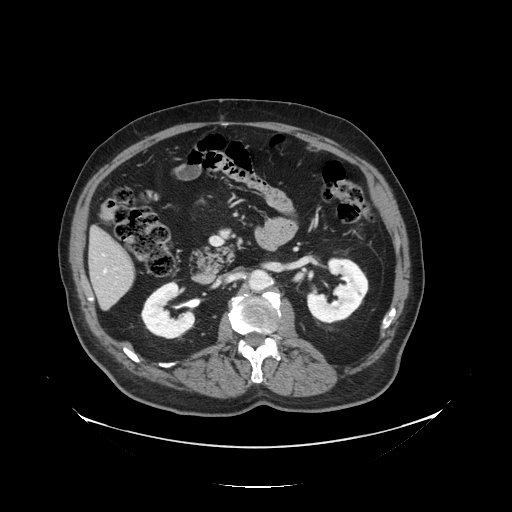
Contrast-enhanced abdominal CT, one axial slice. Position 51 of 138 along the scan axis. Reconstruction kernel STANDARD. 120 kVp. Soft-tissue window (W 400 / L 40 HU). 2.5 mm slice thickness. 512 × 512 image matrix, field of view 497 × 497 mm. Male patient, age 77 years. Case-level facts recorded for this patient, not image findings: diagnosis: colorectal cancer liver metastases, imaged before liver resection; multiple liver metastases: no.
Annotated regions visible in this slice (outlined manually by an expert reader):
- liver: bounding box <91,232,136,309> (left, top, right, bottom; pixels)
- planned liver remnant (the part of the liver to remain after resection): <91,232,134,280>